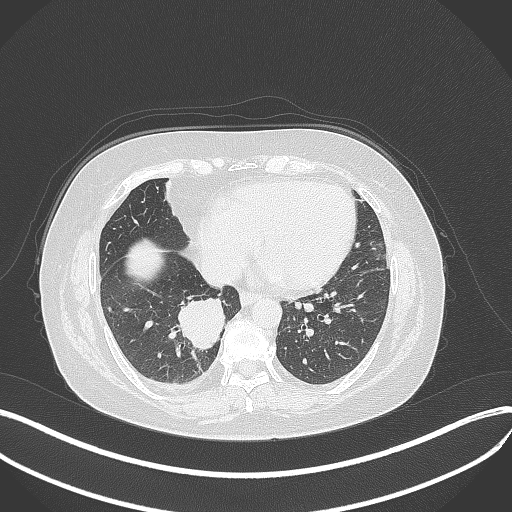
Chest CT, one axial slice; slice 125 of 381 in the series (ordered by position); reconstruction kernel B70f; 120 kVp; lung window (W 1500 / L -600 HU); 1 mm slice thickness; 512 × 512 image matrix, field of view 400 × 400 mm. Female patient, age 56 years. Case-level facts recorded for this patient, not image findings: clinical TNM (as recorded): T2b N1 M0; histopathological grade: G3.
Annotated regions visible in this slice (bounding box drawn by a radiologist):
- lung tumour (recorded histology: small cell carcinoma): bounding box (x1, y1, x2, y2) in pixels: (172, 293, 226, 353)